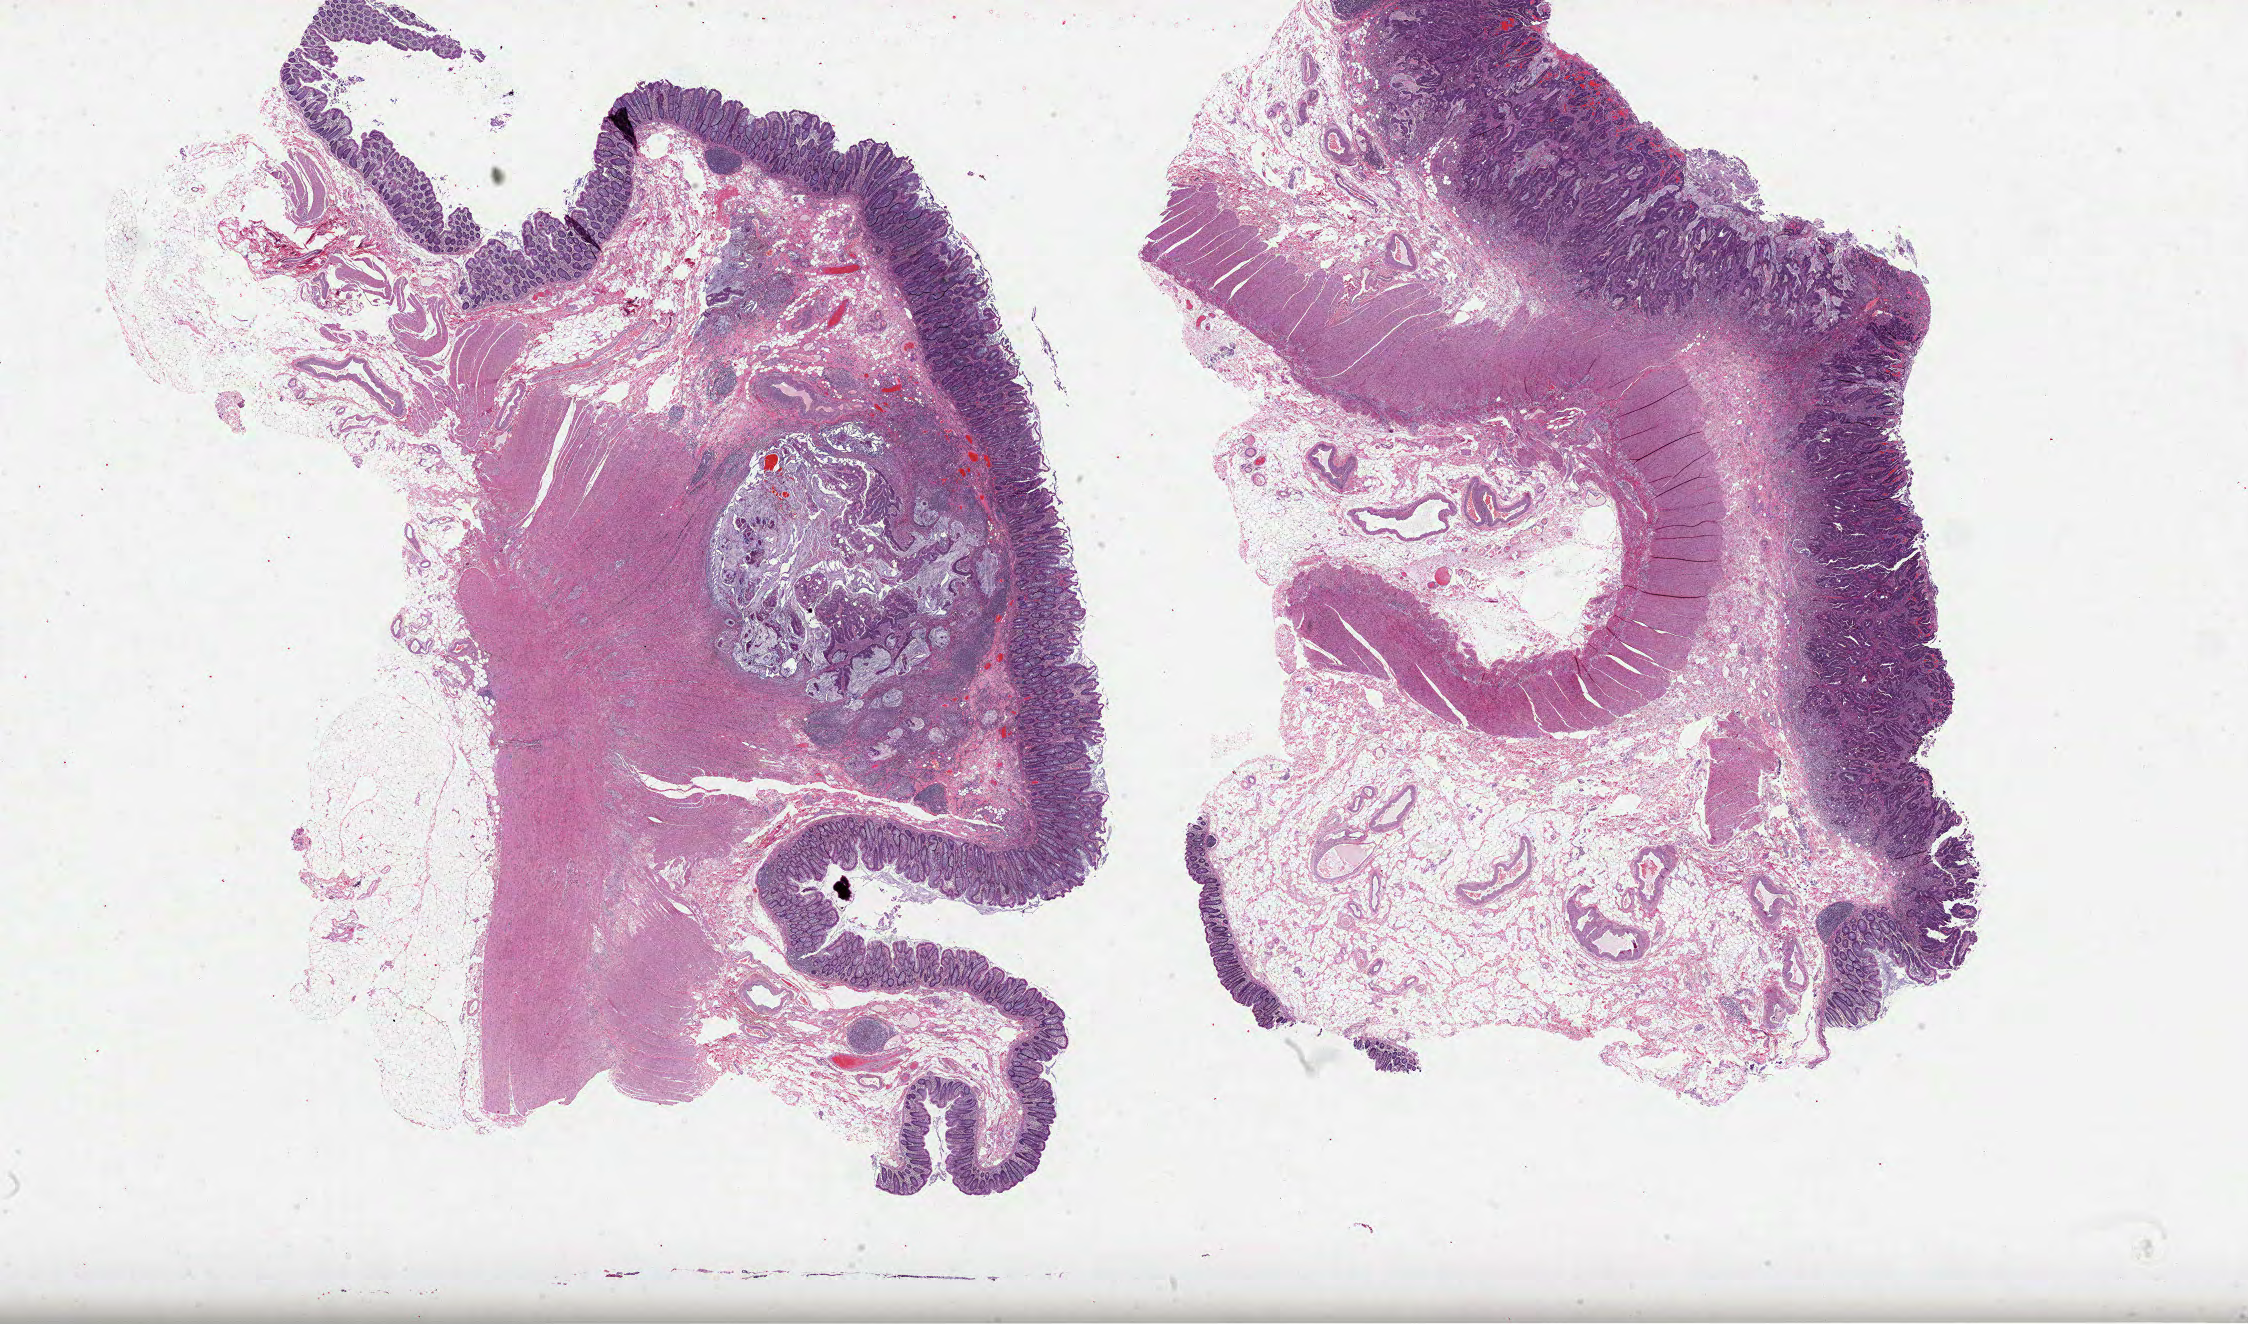
Whole-slide histology image, H&E — shown as a low-resolution overview of the whole scanned area (about 36.3 x 21.4 mm); FFPE section; sample: primary tumour, colon. Female patient; age at initial diagnosis 84 years.
- histologic diagnosis: Adenocarcinoma, NOS (ascending colon)
- AJCC pathologic stage: IIA (7th edition)
- TNM: T3 N0 M0